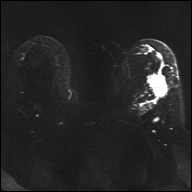
Breast MRI, one axial slice; slice 20 of 32 in the series (ordered by position); diffusion-weighted series; image 2 of 4 stored at this slice position (different b-values; order by instance number); 1.5 T; 4 mm slice thickness; 192 × 192 image matrix. Female patient.
Annotated regions visible in this slice (expert manual segmentation):
- tumour on diffusion-weighted imaging: bounding box (x1, y1, x2, y2) in pixels: (149, 76, 167, 95)